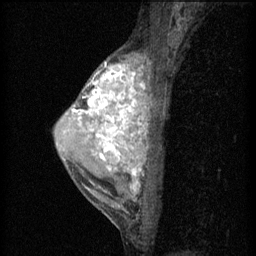
Breast MRI (dynamic contrast-enhanced), one sagittal slice. Position 37 of 60 along the scan axis. 3 images stored at this slice position (order not interpretable as contrast timing). 1.5 T. TE 4.2 ms, TR 11 ms. 2 mm slice thickness. 256 × 256 image matrix, field of view 180 × 180 mm. Patient: female, 40 years.
Structures marked on this image (semi-automatically segmented with operator editing):
- analysis volume of interest (the breast-tissue region the enhancement analysis was run in; not a lesion): bounding box (x1, y1, x2, y2) in pixels: (55, 54, 153, 203)
- tumour enhancement mask (voxels above the 70 % enhancement threshold inside the analysis volume of interest): (73, 62, 149, 191)